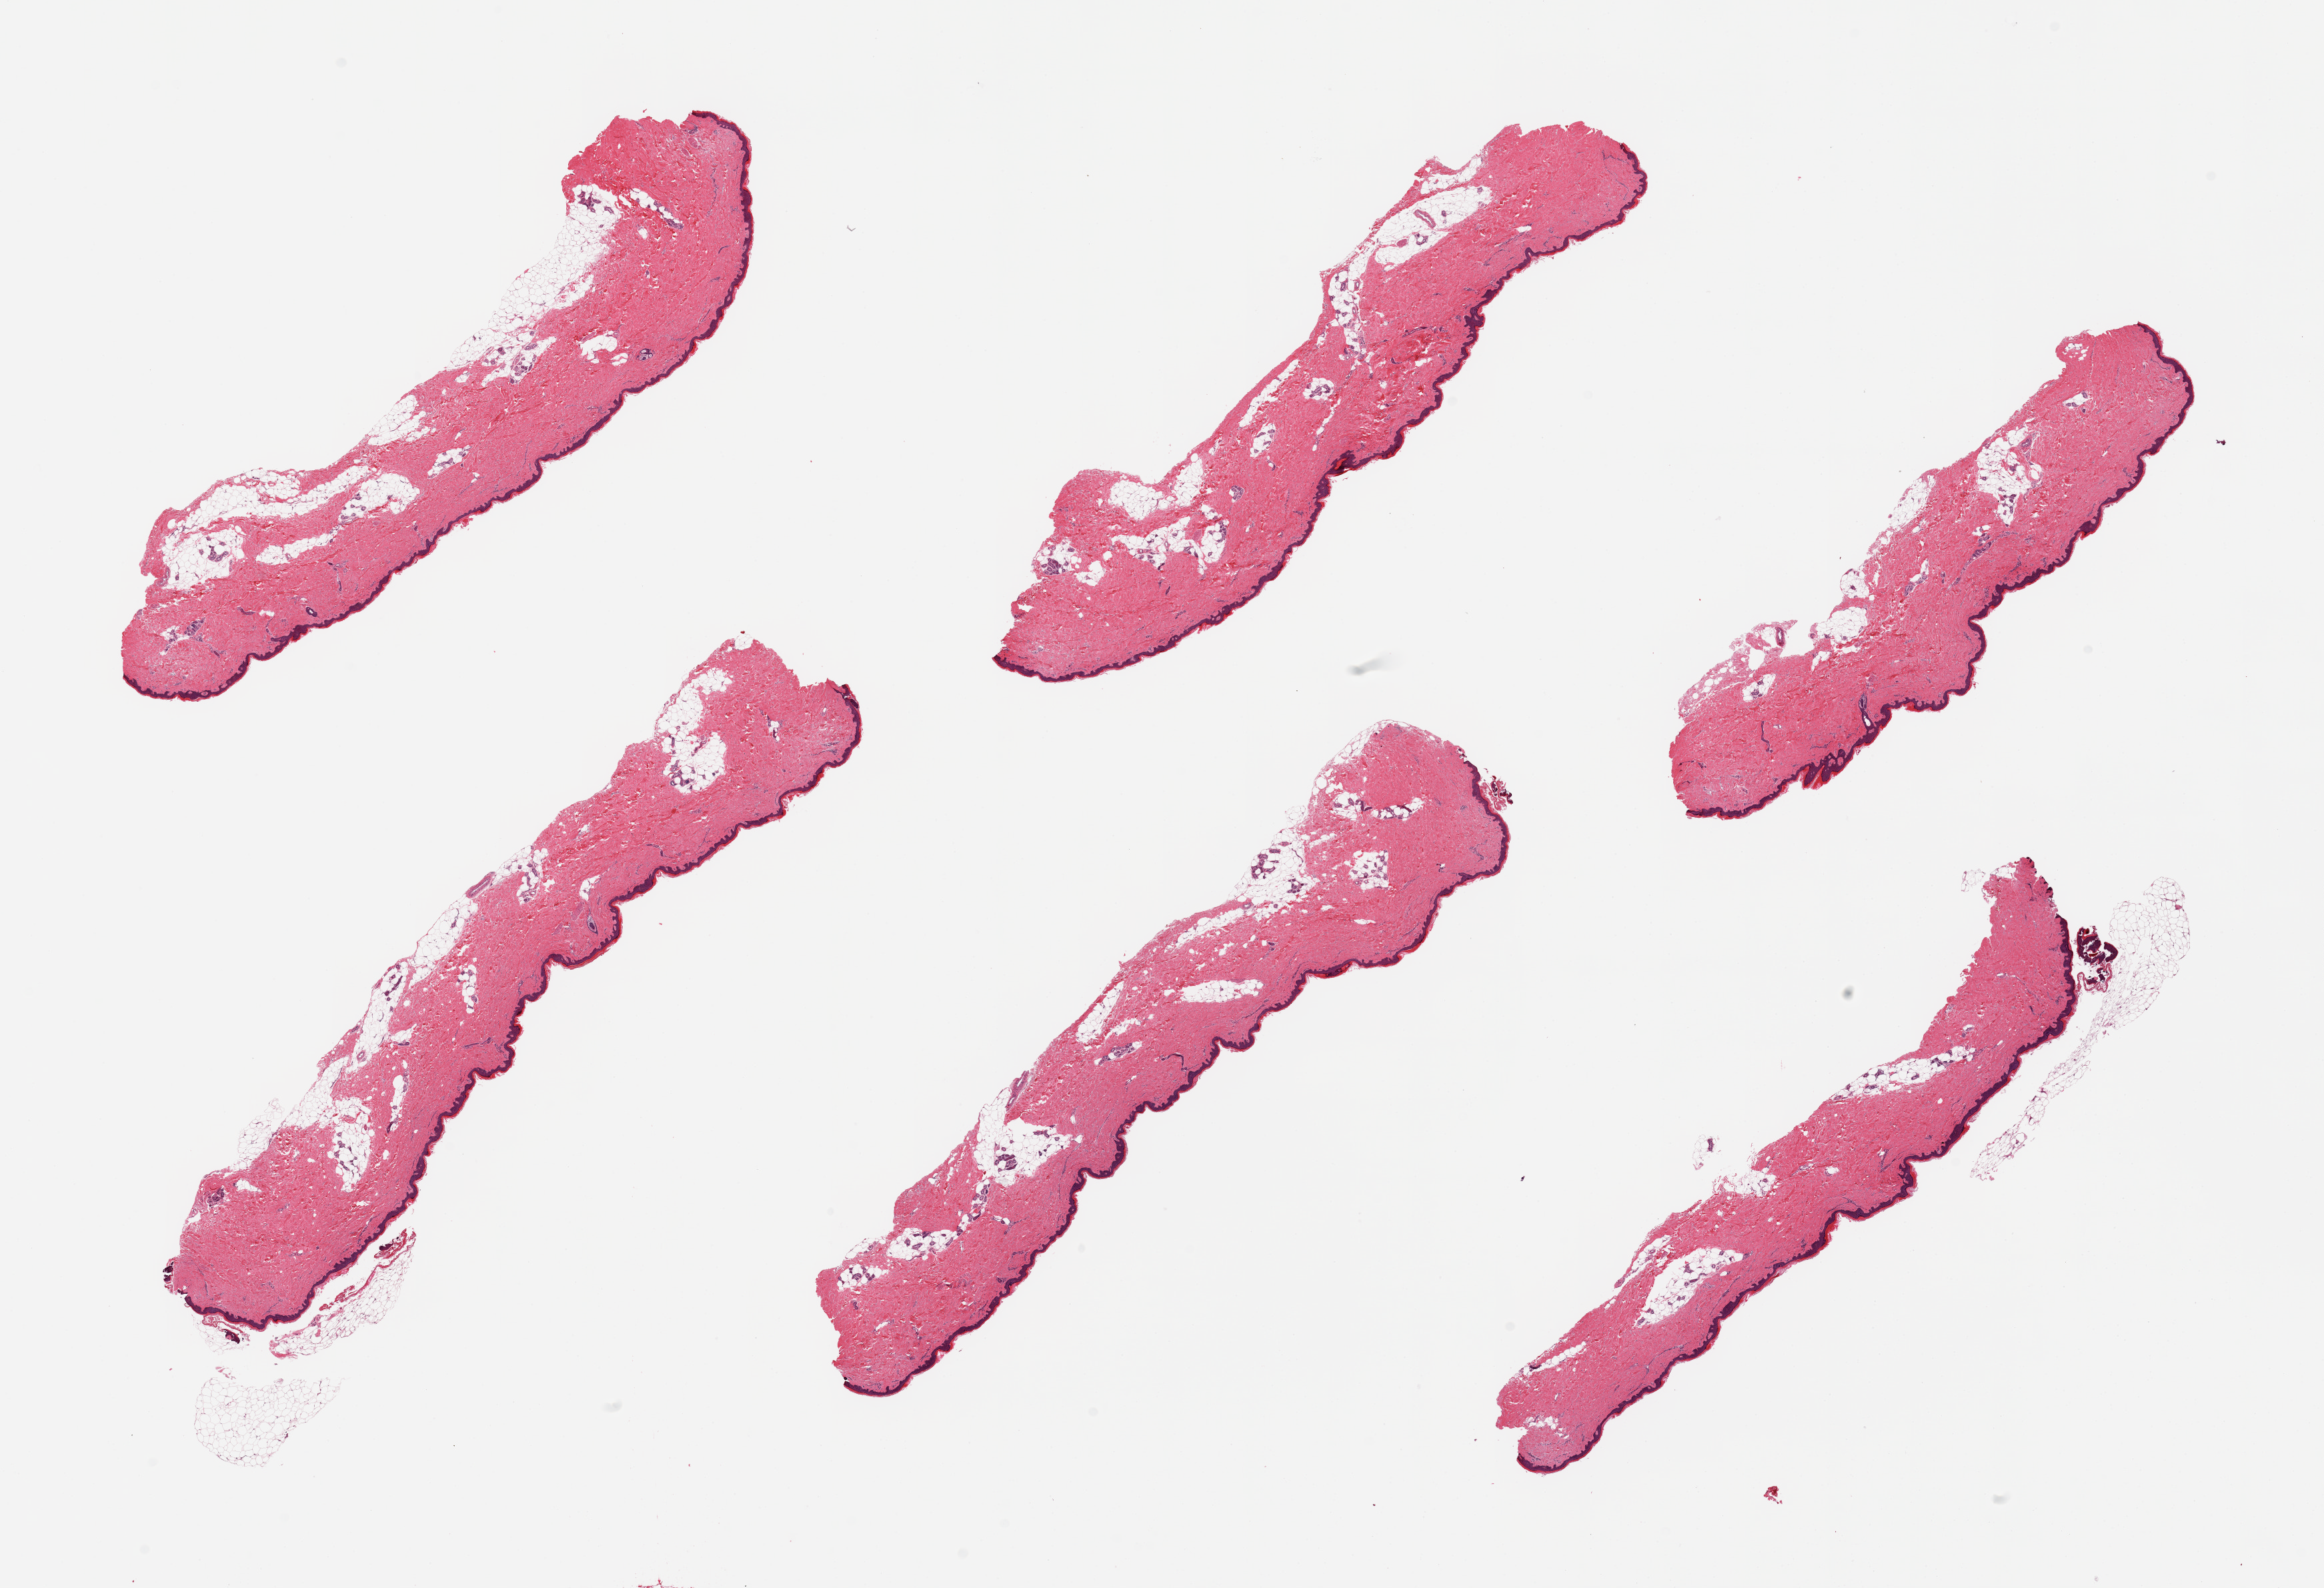
H&E whole-slide image, low-resolution overview of the scanned area, about 27.6 x 18.8 mm, PAXgene-fixed paraffin-embedded (PFPE) section, target tissue: skin of lower leg, donor tissue sample.
Pathologist's review note for this sample: 6 pieces, no signifcnt dermal fat, squamous epithelium is ~55-60 microns.